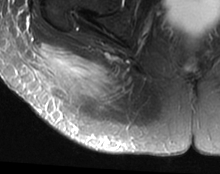
MRI of an extremity soft-tissue mass, one axial slice; position 15 of 63 along the scan axis; T2-weighted fat-saturated; MR volume resampled by the dataset authors to the PET/CT grid (not the native acquisition matrix); 3.27 mm slice thickness; 220 × 174 image matrix, field of view 215 × 170 mm. Female patient. From the clinical record (not read from this slice): histological type: spindle cell suggestive of myxofibrosarcoma; grade: intermediate; site of the primary tumour: right buttock.
Outlined on this slice (expert contour drawn on MRI and transferred to this co-registered scan by the dataset authors):
- gross tumour volume (mass): bounding box <38,45,117,105> (left, top, right, bottom; pixels)